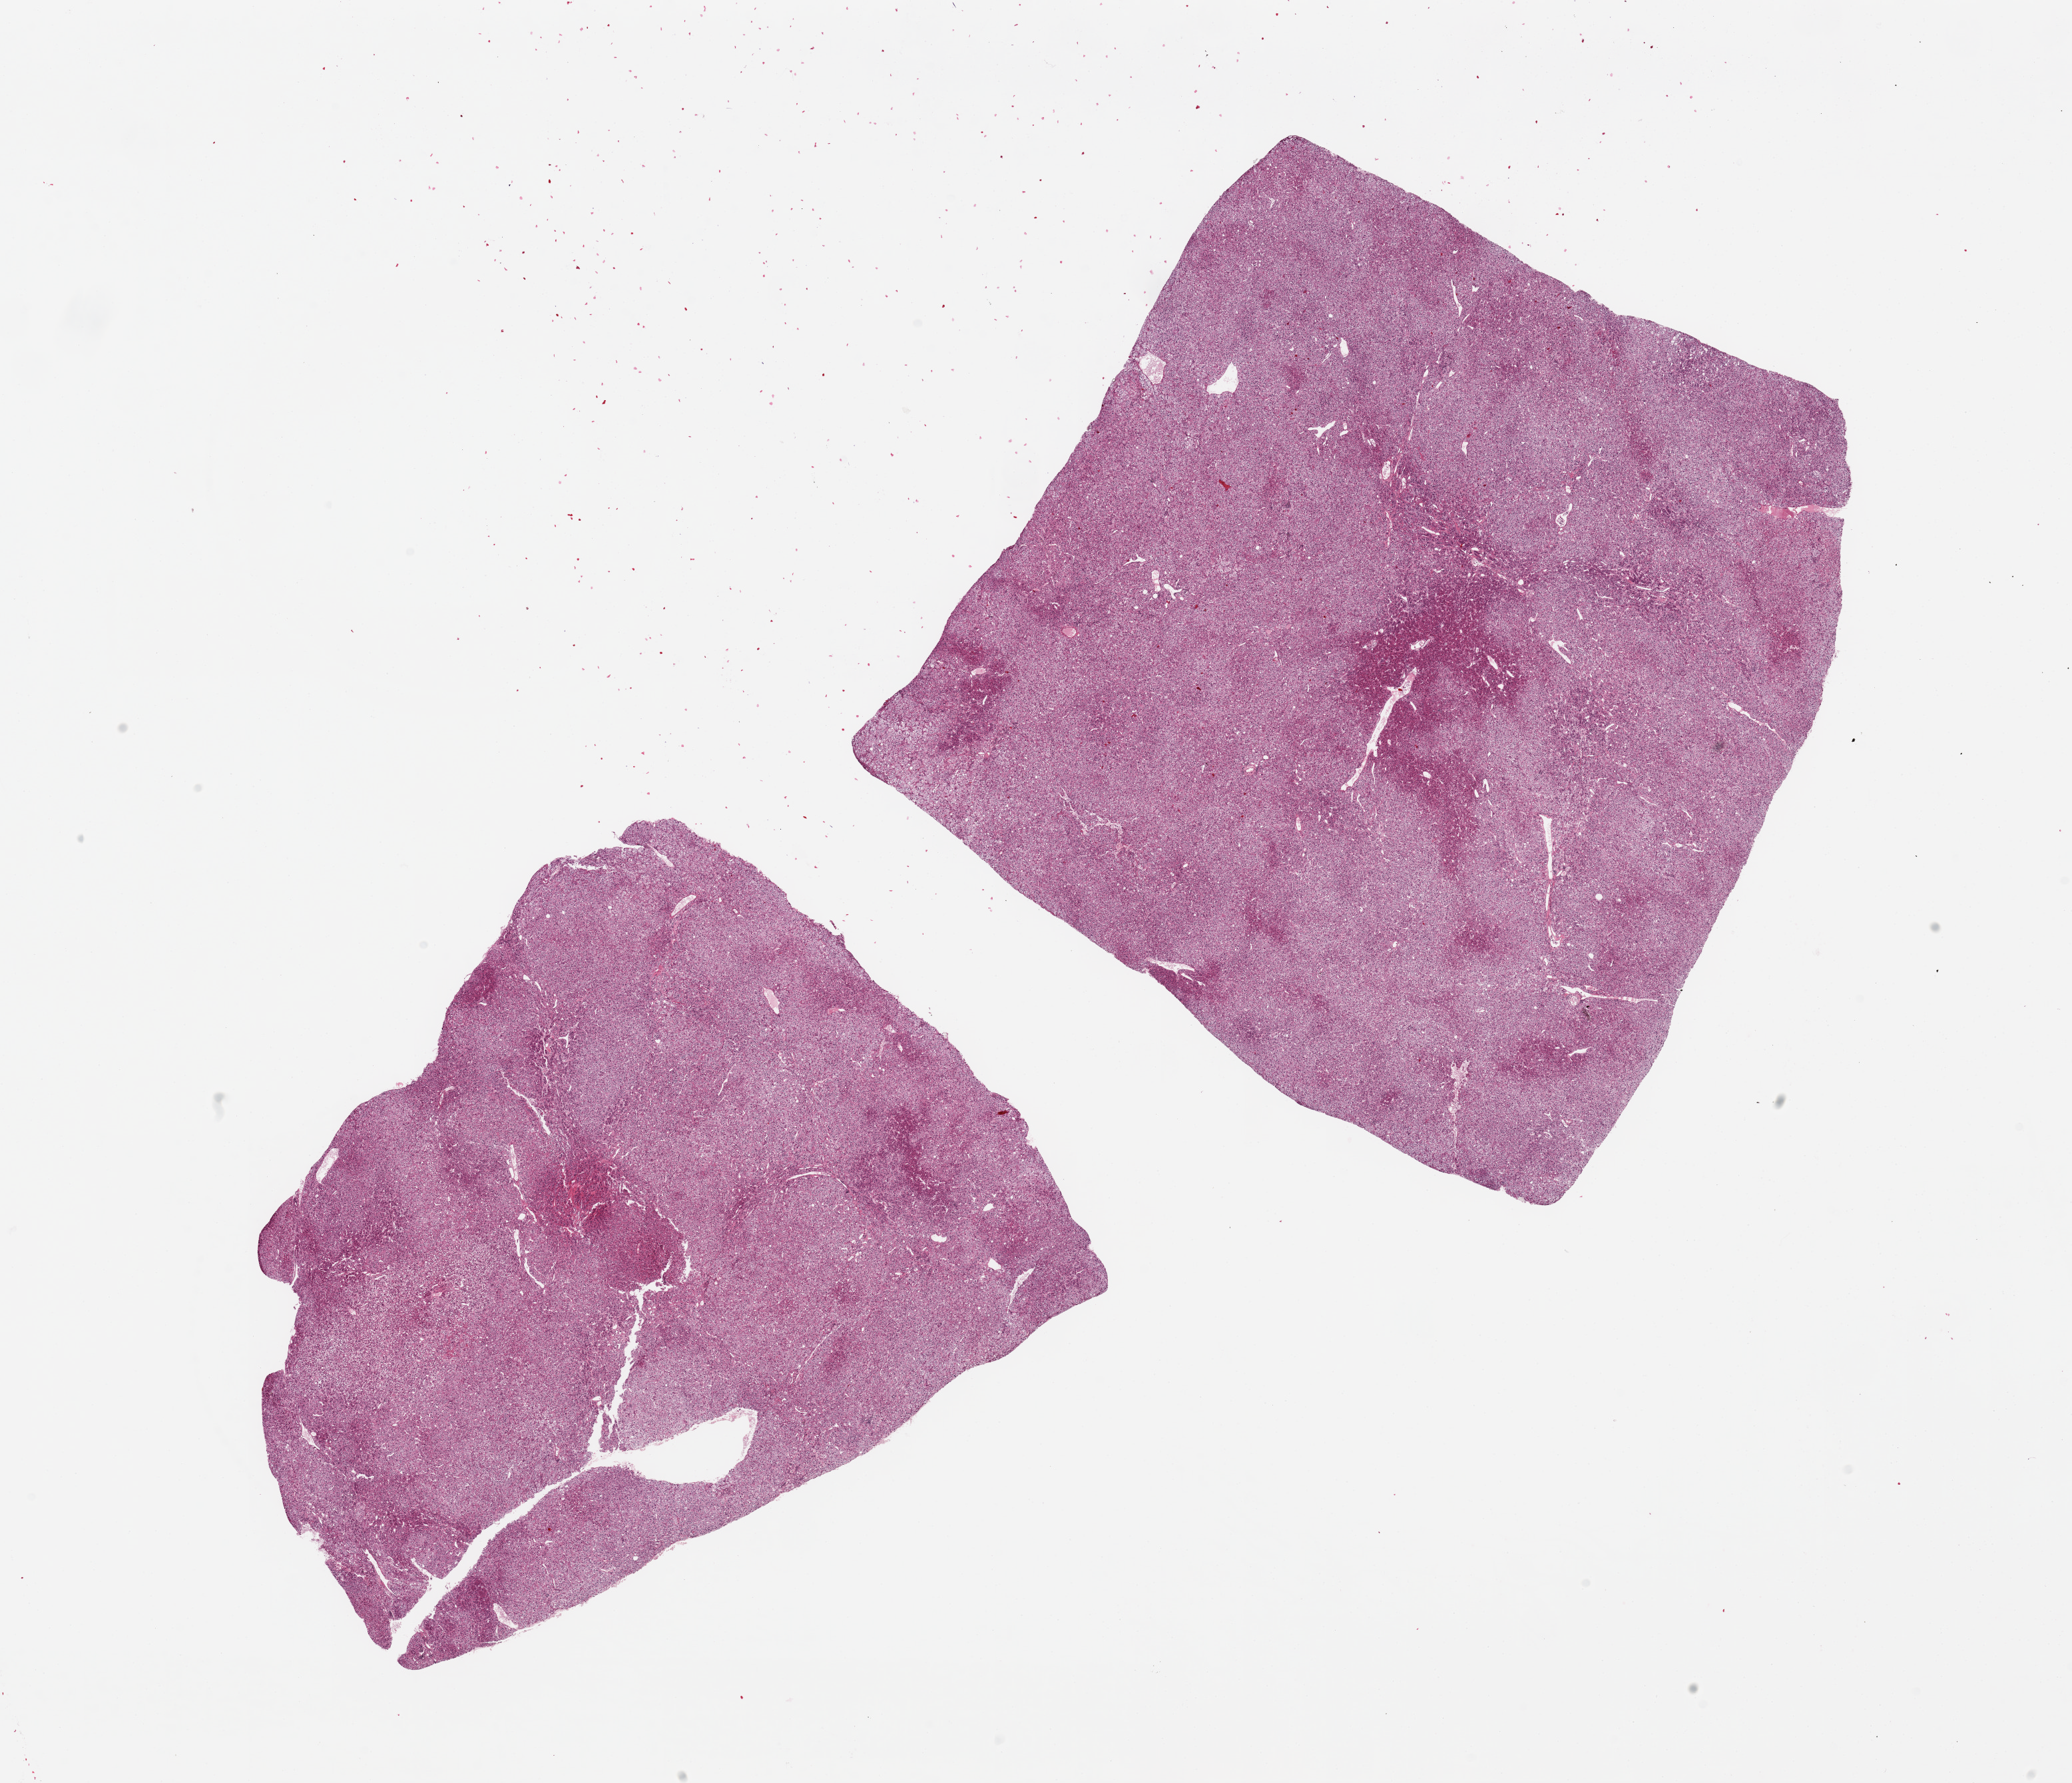
Whole-slide image, haematoxylin and eosin stain, brightfield, low-resolution overview of the scanned area, about 24.6 x 21.2 mm (acquisition: 20x scan); PAXgene-fixed, paraffin-embedded tissue; target tissue: adrenal gland; tissue donor sample. Donor sex: female.
Reviewer comment on this tissue sample: 2 pieces, 10x8 & 10x10mm; all cortex; well preserved.